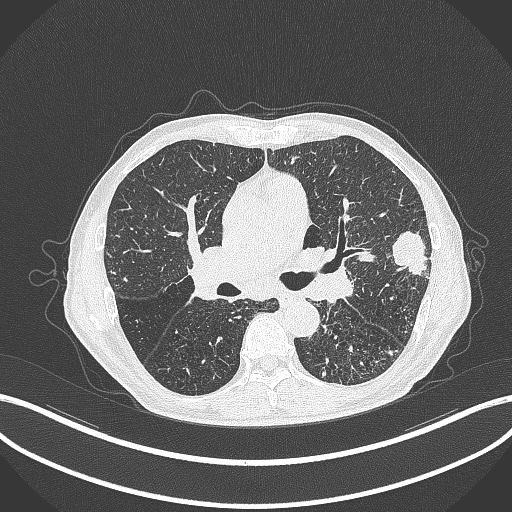
Chest CT, one axial slice; position 239 of 463 along the scan axis; 120 kVp; lung window (W 1500 / L -600 HU); 1 mm slice thickness; 512 × 512 image matrix, field of view 400 × 400 mm. Male patient, age 74 years. Case-level facts recorded for this patient, not image findings: clinical TNM (as recorded): T2a N1 M0.
Annotated regions visible in this slice (rectangle marked by the reading radiologist):
- lung tumour (recorded histology: adenocarcinoma): bounding box [x1, y1, x2, y2] px = [390, 227, 429, 278]